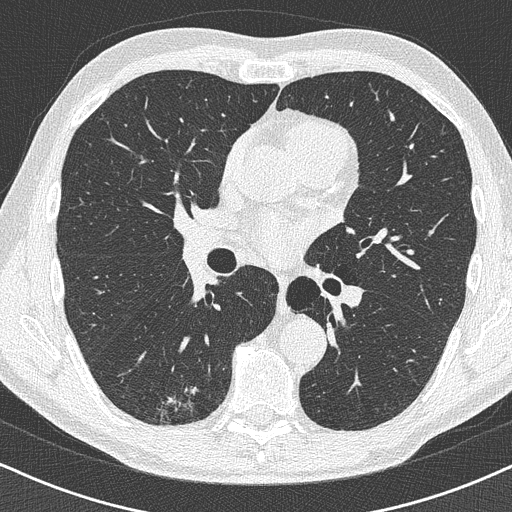
Chest CT (low-dose screening protocol), one axial image, baseline screening round, lung window (W 1500 / L -600 HU), lung (sharp) reconstruction kernel (B50f), 120 kVp, slice 202 of 438 in the series, 512 × 512 image matrix, field of view 320 × 320 mm. Male participant, aged 63 years at enrolment. Former smoker at enrolment.
Expert-annotated lung lesion, box from (x=141, y=378) to (x=212, y=431) px. Screening reader's record for this exam (one nodule recorded; not confirmed to be the boxed lesion): non-calcified nodule or mass ≥4 mm, right lower lobe, 16 × 13 mm, poorly defined margins.